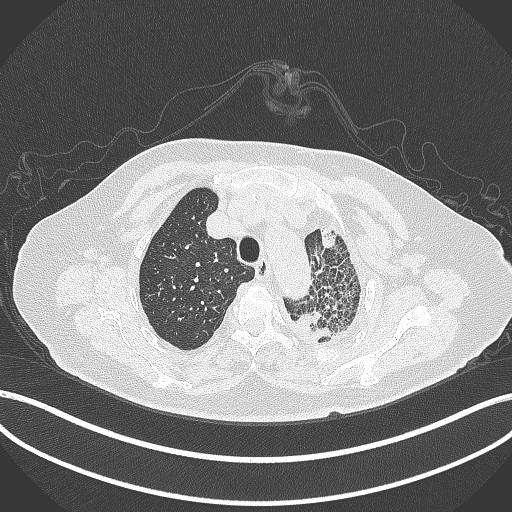
Chest CT, one axial slice; position 318 of 399 along the scan axis; 120 kVp; lung window (W 1500 / L -600 HU); 1 mm slice thickness; 512 × 512 image matrix, field of view 400 × 400 mm. Patient: female, 75 years. From the clinical record (not read from this slice): clinical TNM (as recorded): T3 N3 M1.
Structures marked on this image (rectangle marked by the reading radiologist):
- lung tumour (recorded histology: adenocarcinoma): box from (x=293, y=304) to (x=340, y=345) px